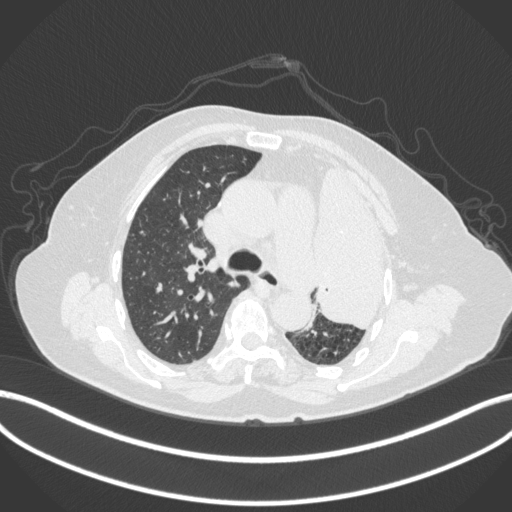
Chest CT, one axial slice. Slice 261 of 399 in the series (ordered by position). 120 kVp. Lung window (W 1500 / L -600 HU). 1 mm slice thickness. 512 × 512 image matrix, field of view 400 × 400 mm. Patient: female, 75 years. Case-level facts recorded for this patient, not image findings: clinical TNM (as recorded): T3 N3 M1.
Outlined on this slice (bounding box drawn by a radiologist):
- lung tumour (recorded histology: adenocarcinoma): box from (x=309, y=157) to (x=401, y=341) px